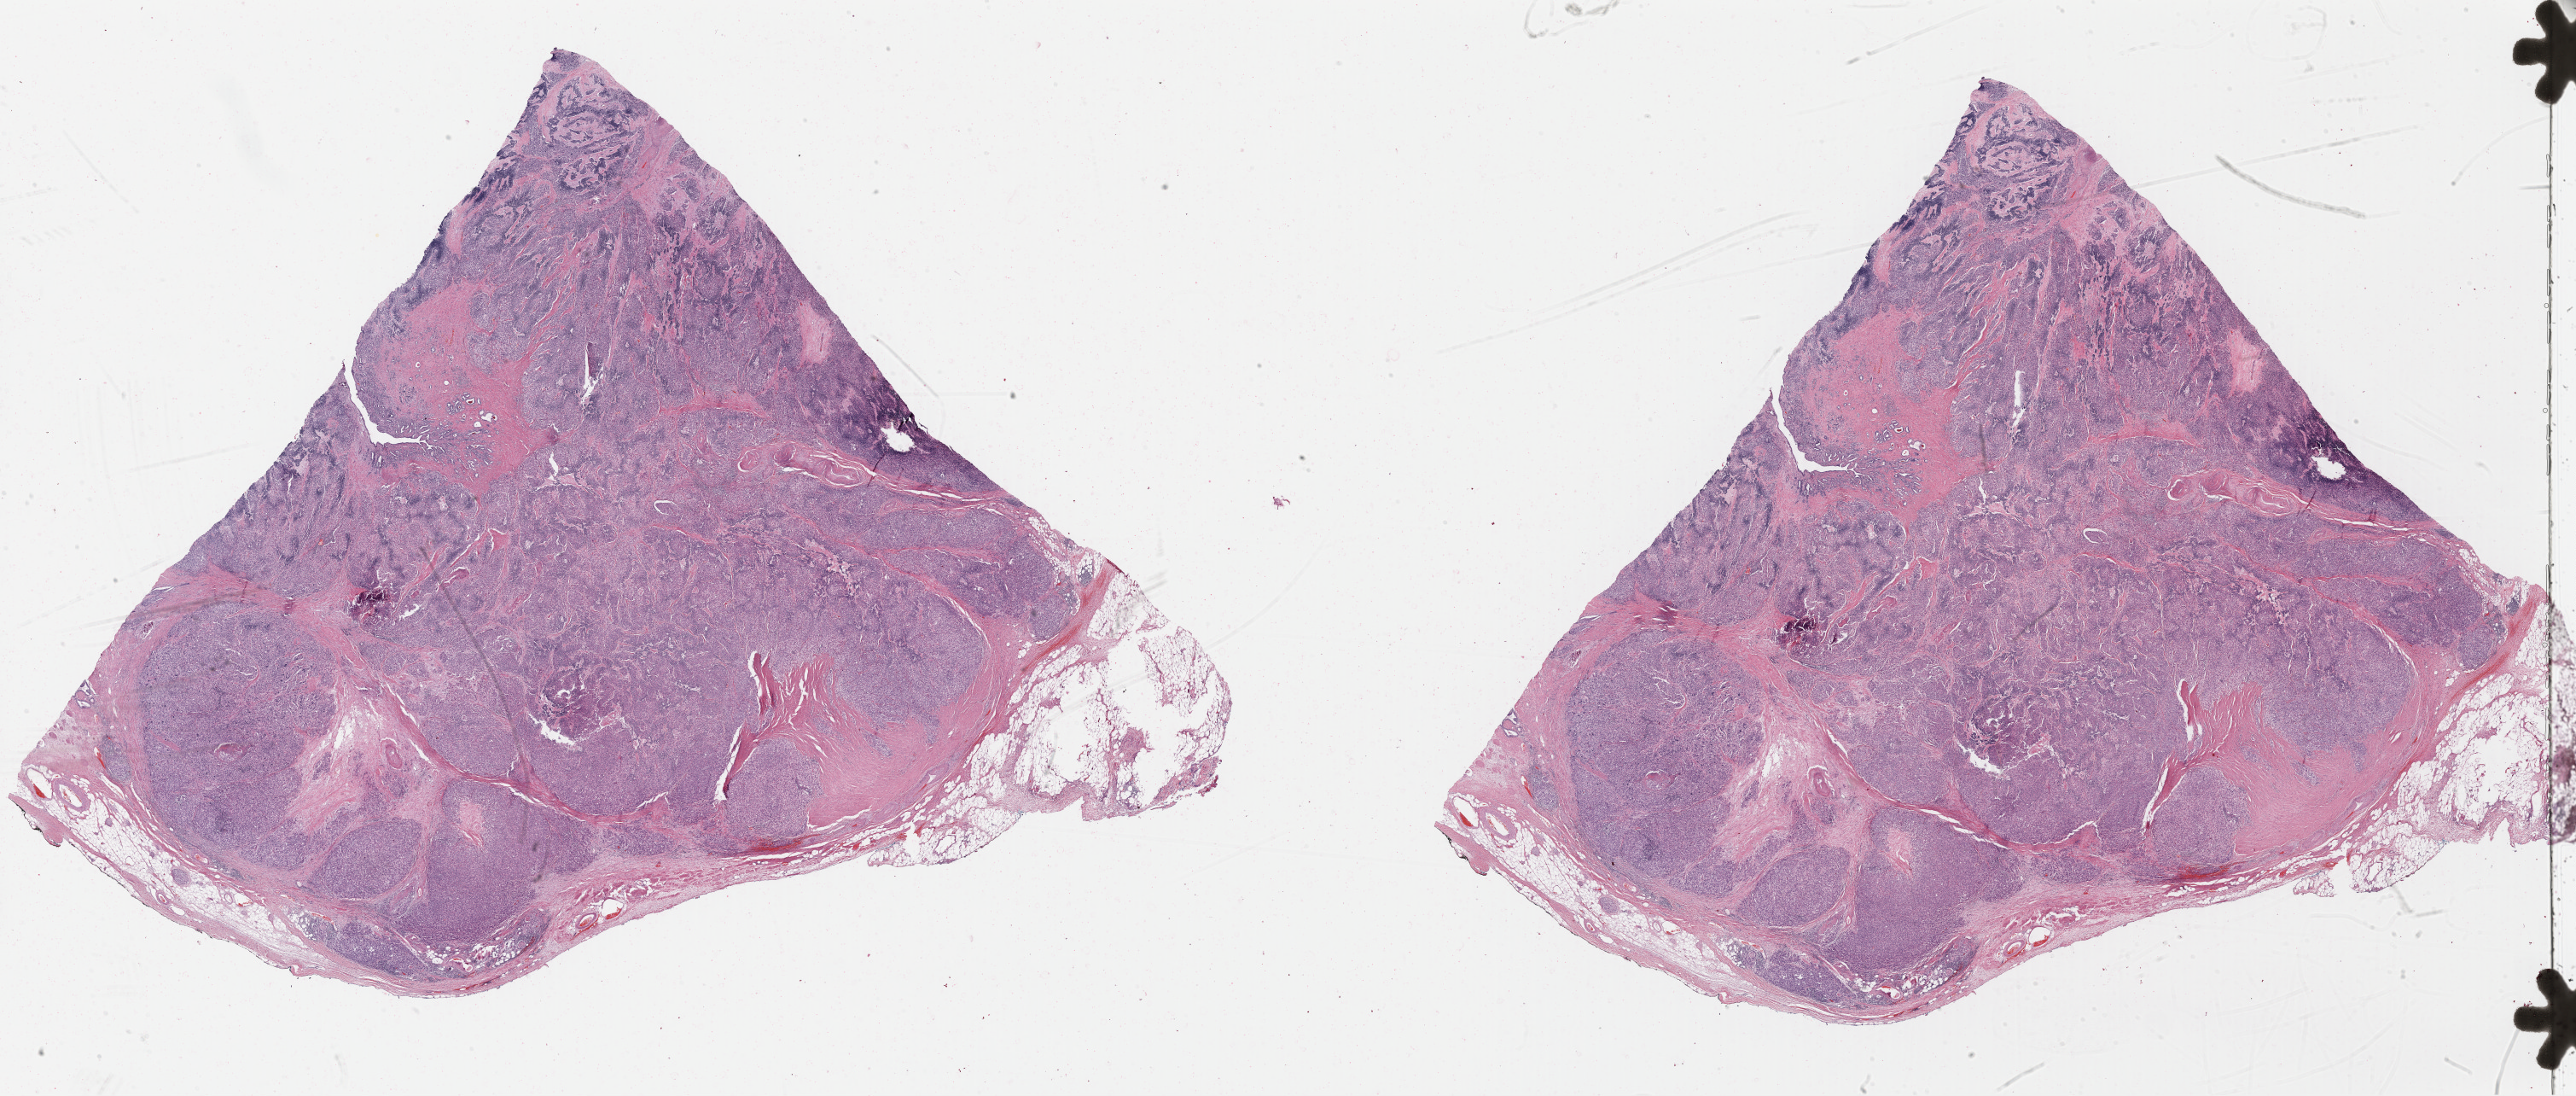
H&E whole-slide image, a low-resolution overview of the entire scanned area, about 47.5 x 20.2 mm (acquisition: 40x scan), FFPE section, primary tumour sample from the bladder. Patient: male, age at initial diagnosis 83 years. Histologic grade: high grade.
AJCC pathologic stage: II. Lymph nodes positive (case pathology): 0 of 5 examined. Pathologic diagnosis: Transitional cell carcinoma.